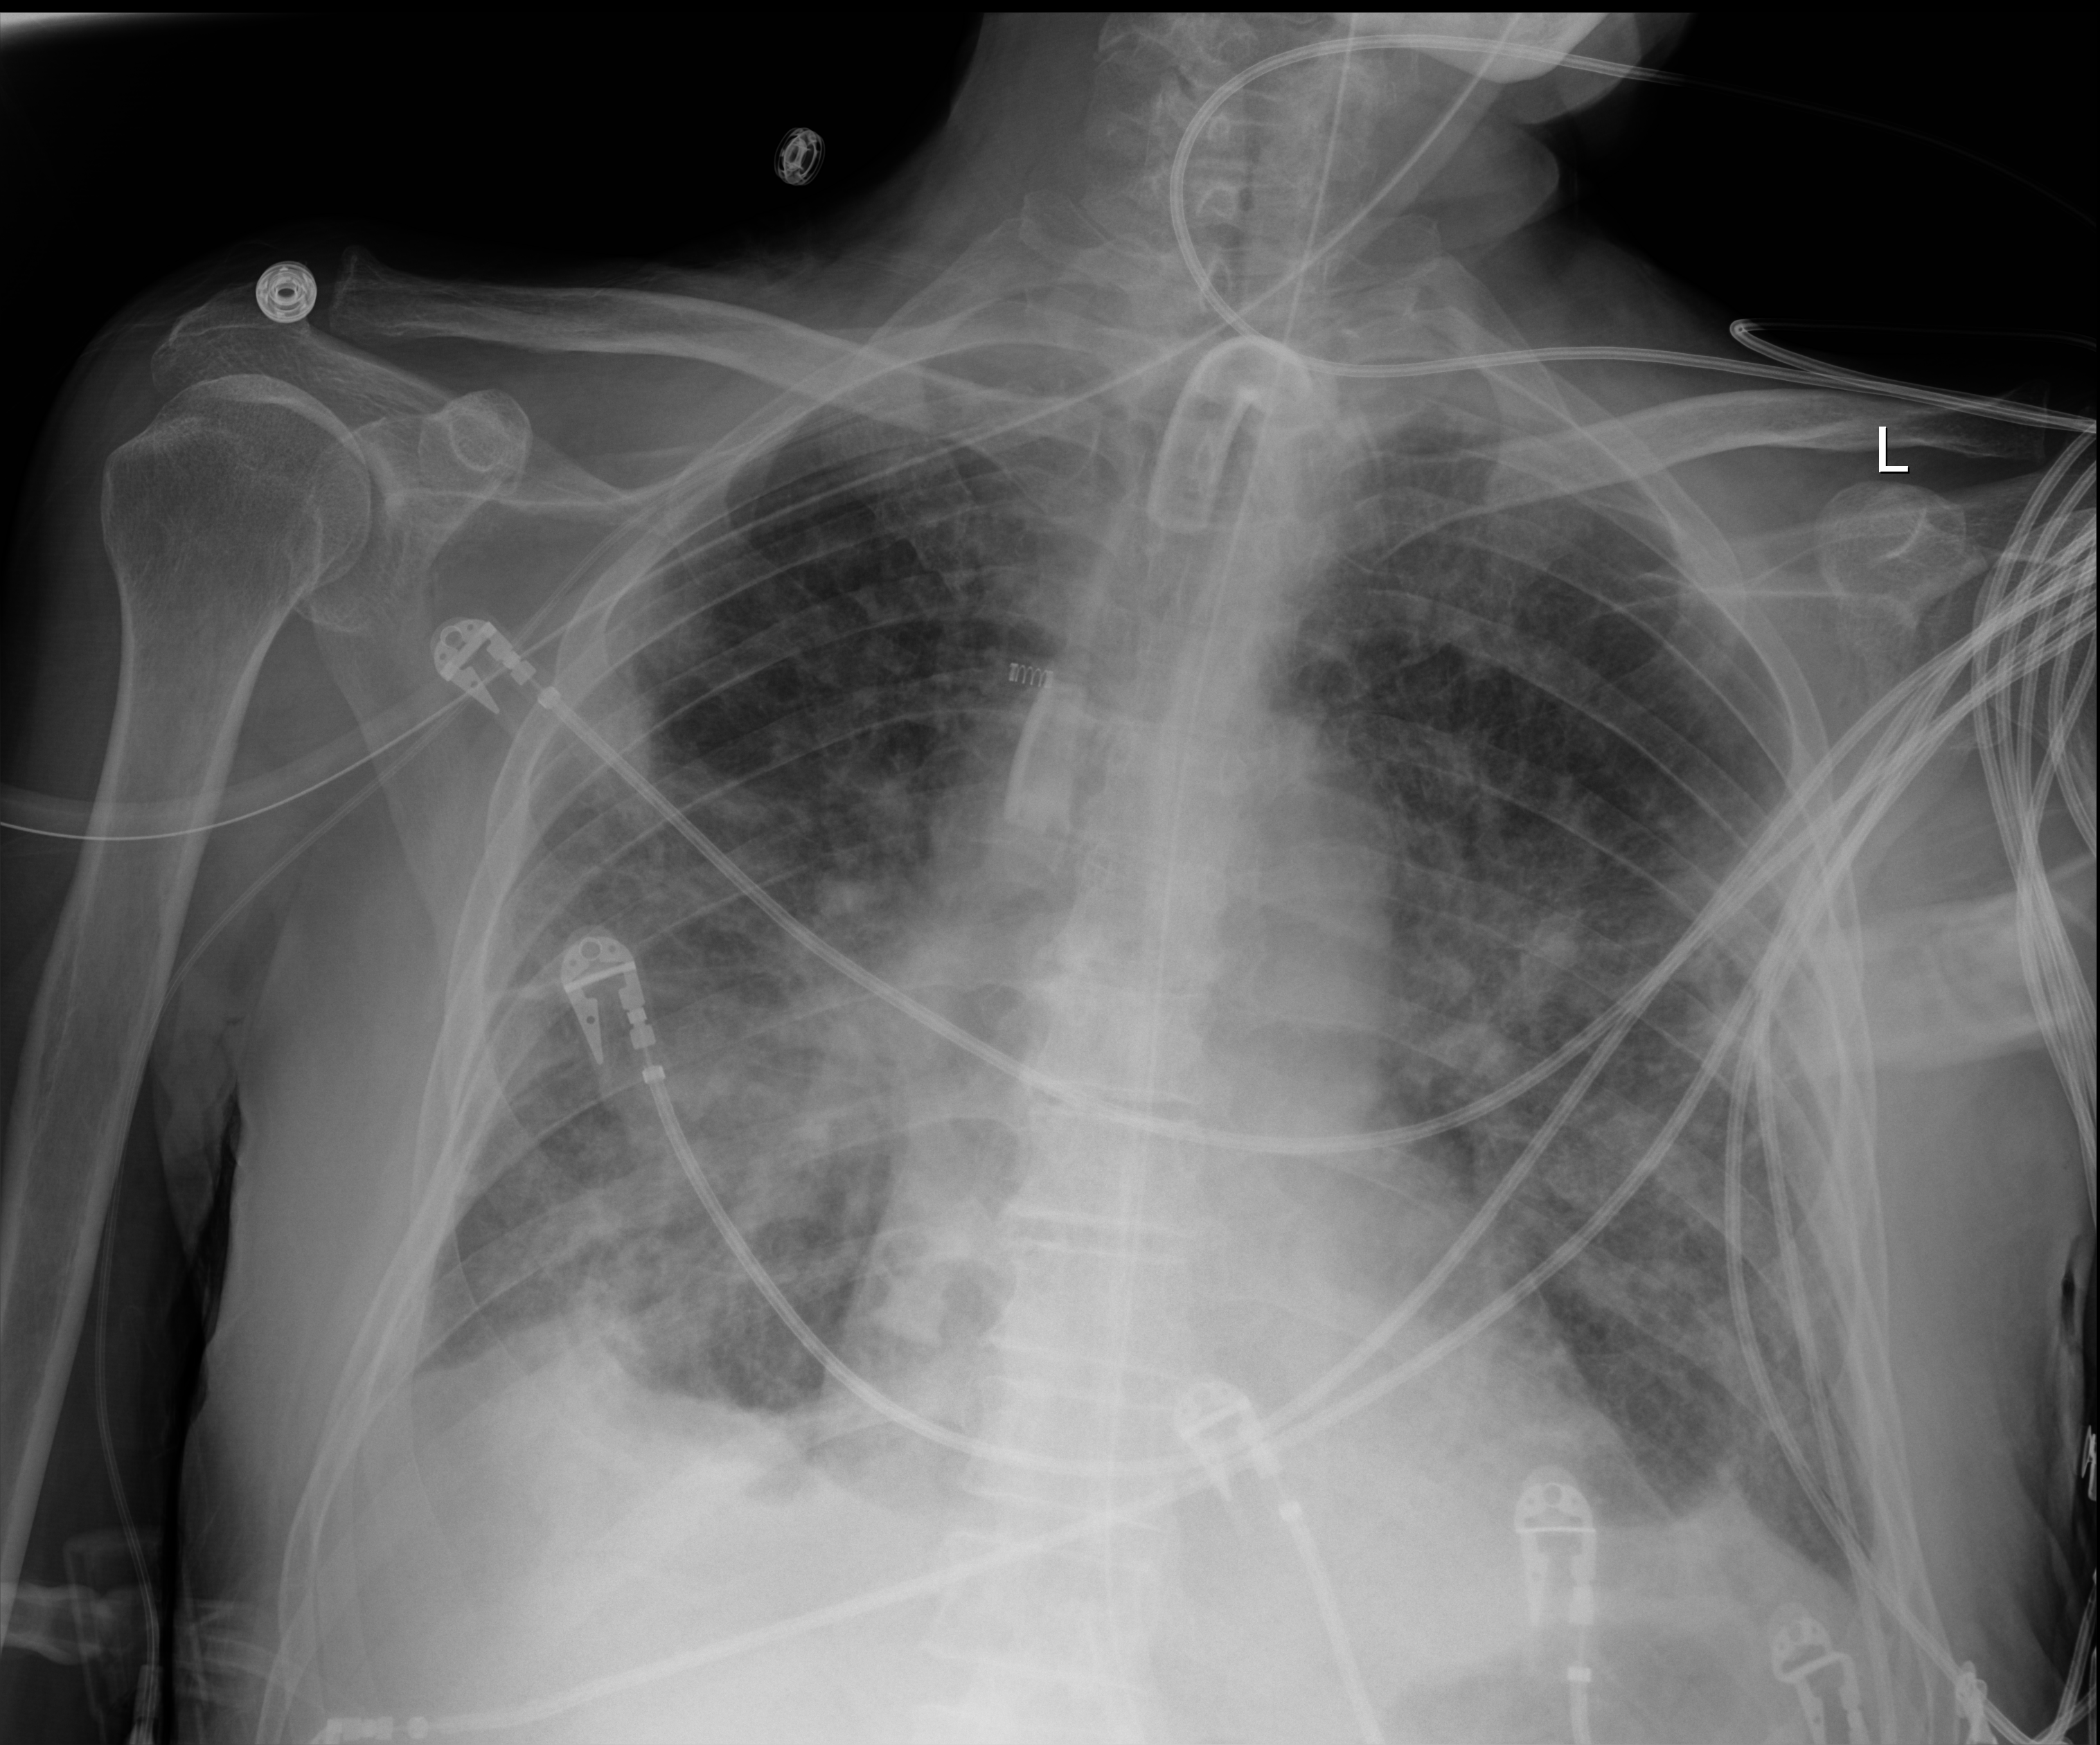
Bedside chest radiograph (digital radiography); anteroposterior (AP) projection. Patient hospitalised with COVID-19; male, aged 75–90 years.
From the hospital-stay record, not from the radiograph (when in the stay this image was taken is not recorded):
- smoking status (admission record): never
- mechanically ventilated during this hospital stay: yes
- COPD (admission record): no